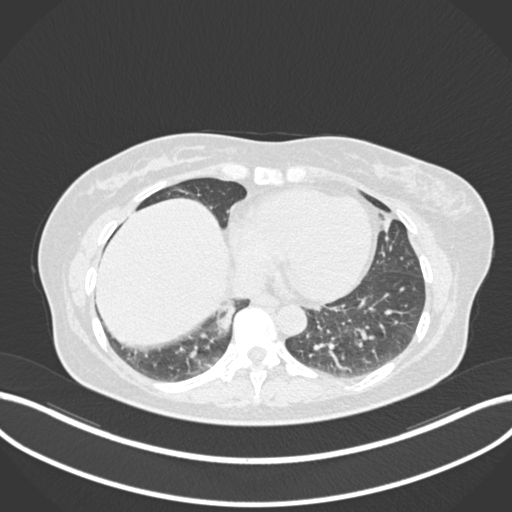
Chest CT, one axial slice; slice 542 of 677 in the series (ordered by position); lung window (W 1500 / L -600 HU); 1 mm slice thickness; 512 × 512 image matrix. Female patient, age 54 years. Case-level facts recorded for this patient, not image findings: clinical TNM (as recorded): T4 N0 M0.
Annotated regions visible in this slice (bounding box drawn by a radiologist):
- lung tumour (recorded histology: adenocarcinoma): box from (x=208, y=300) to (x=242, y=340) px